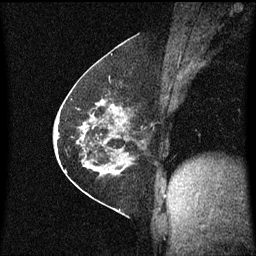
Breast MRI (dynamic contrast-enhanced), one sagittal slice. Slice 32 of 60 in the series (ordered by position). Dynamic contrast-enhanced series, image 2 of 3 at this slice position (ordered by acquisition). 1.5 T. TE 4.2 ms, TR 8.4 ms. 2 mm slice thickness. 256 × 256 image matrix, field of view 200 × 200 mm. Patient: female, 60 years.
Structures marked on this image (semi-automatic segmentation, software-assisted and operator-edited):
- analysis volume of interest (the breast-tissue region the enhancement analysis was run in; not a lesion): bounding box <69,66,146,193> (left, top, right, bottom; pixels)
- tumour enhancement mask (voxels above the 70 % enhancement threshold inside the analysis volume of interest): <69,70,139,171>